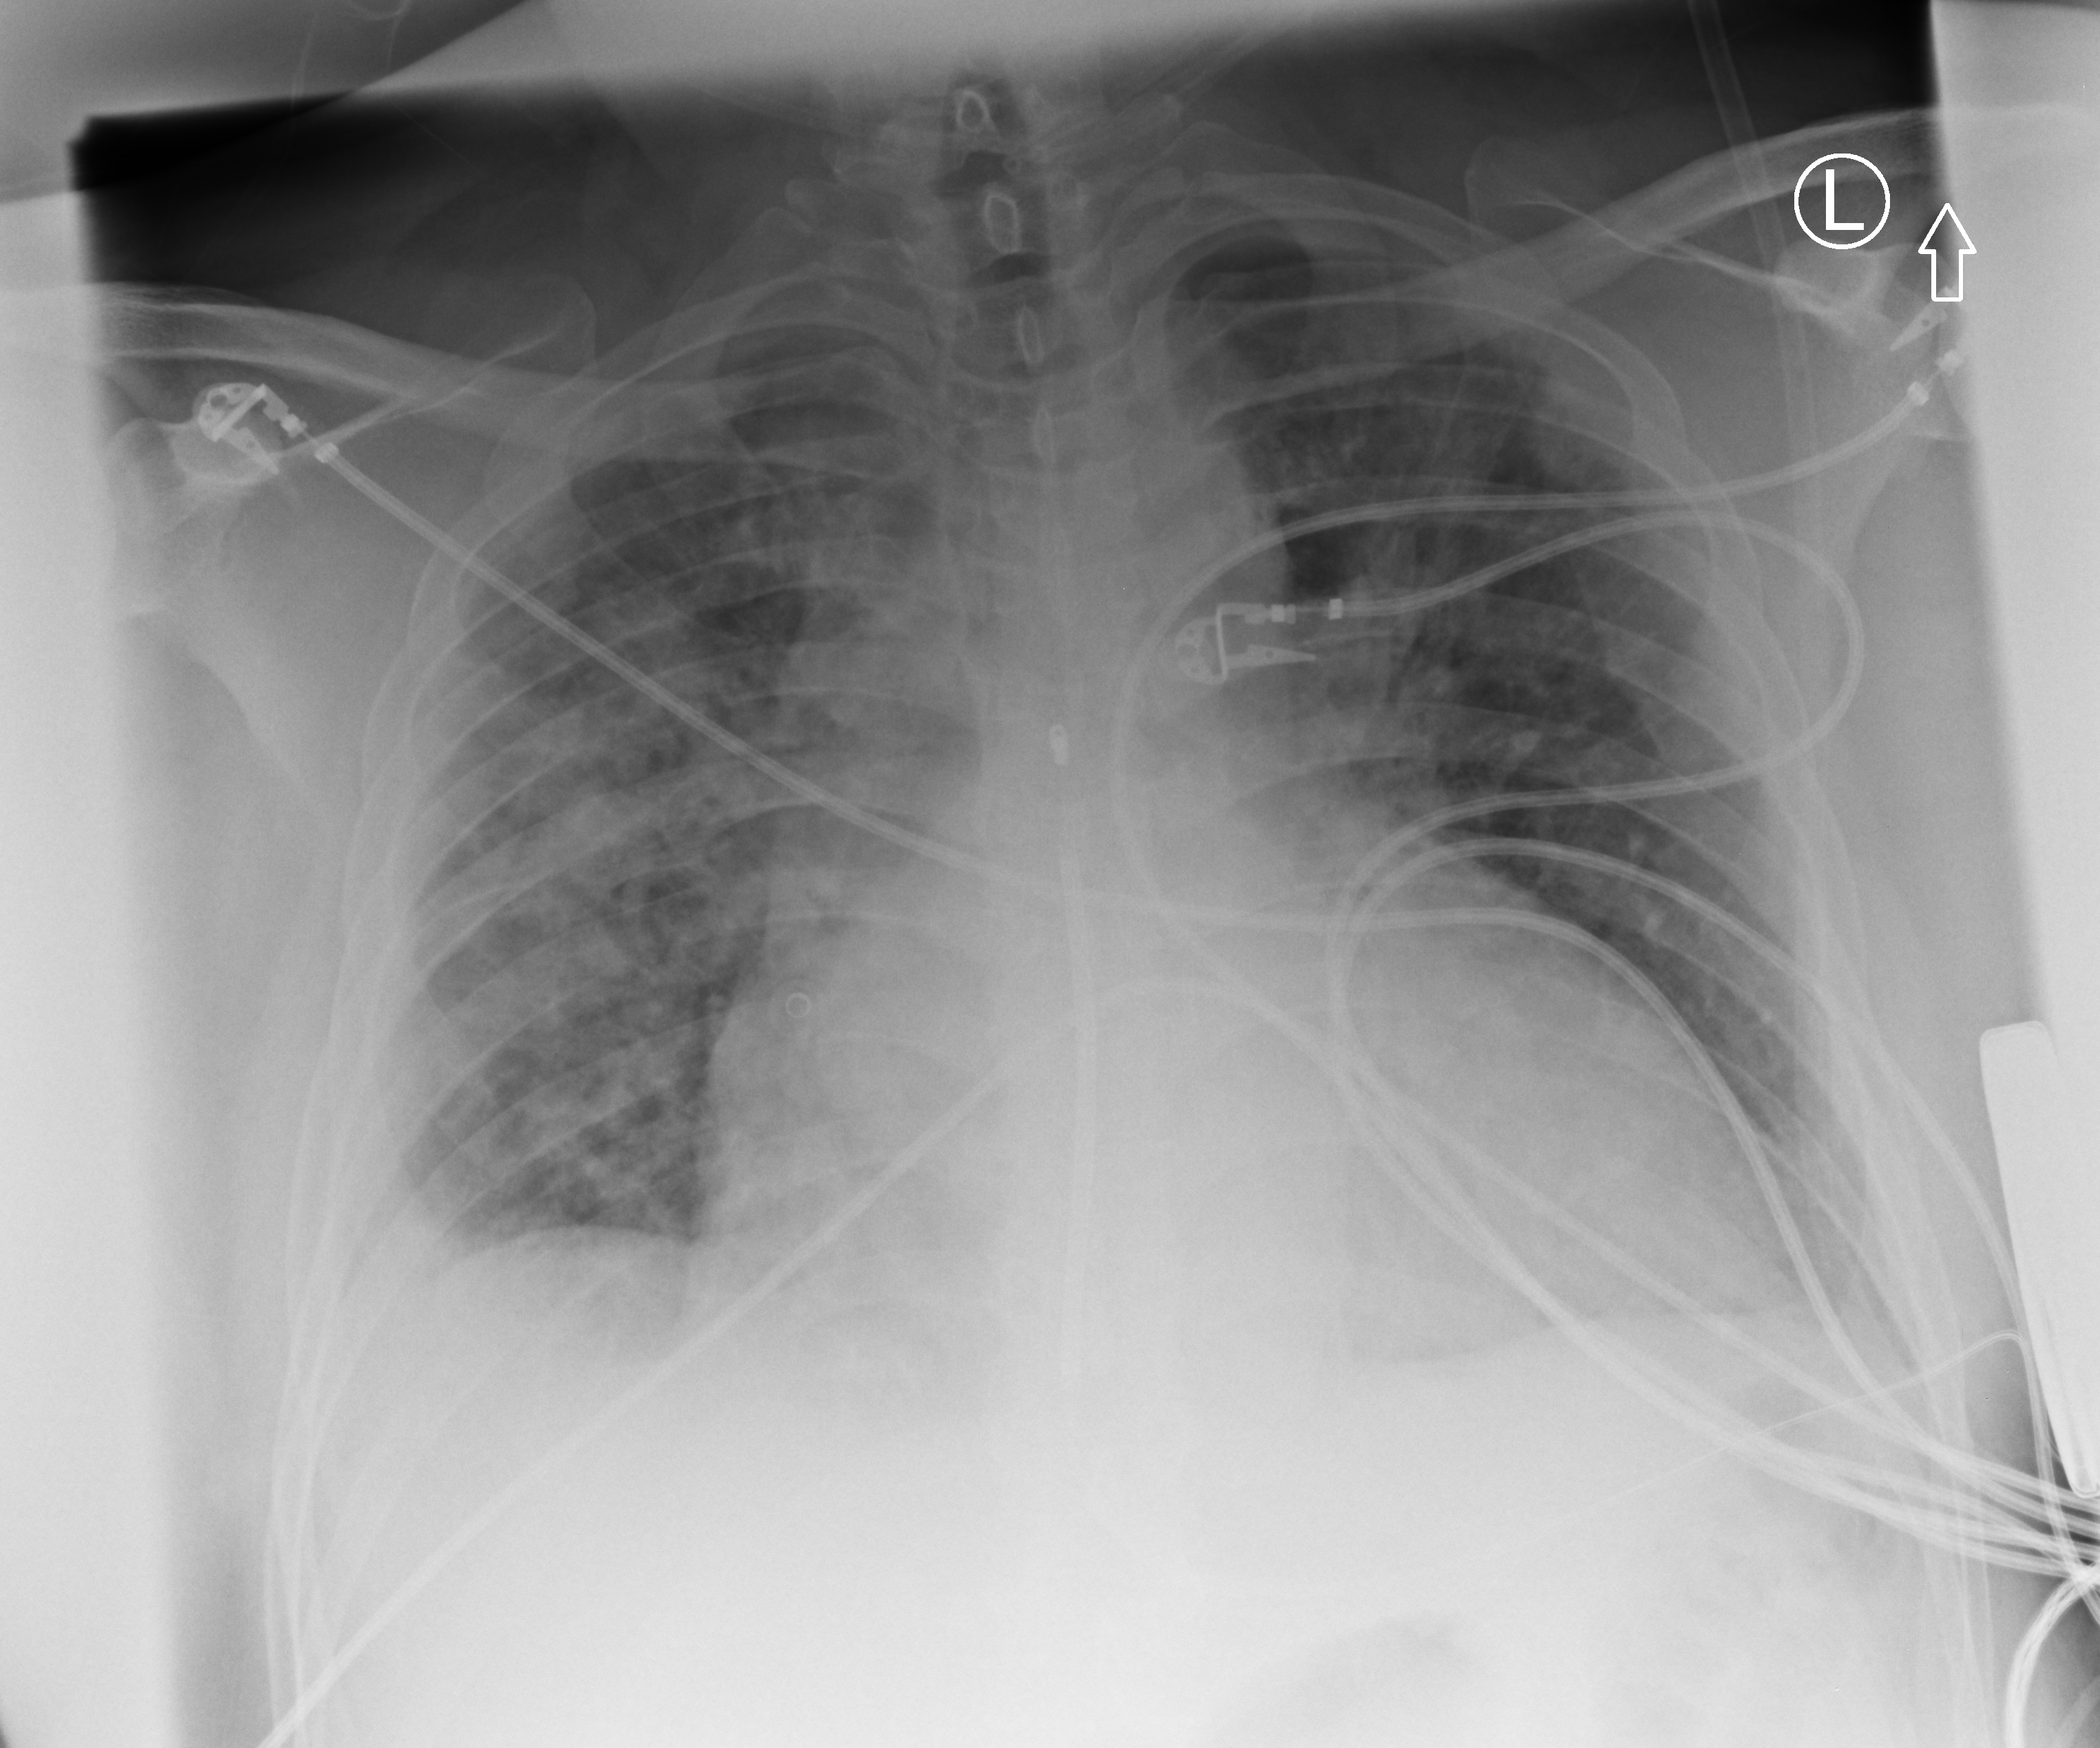
Chest X-ray (portable), anteroposterior (AP) projection. Patient hospitalised with COVID-19; male, aged 18–59 years.
Admission-level facts for this patient (not findings on this image; timing relative to this image not recorded):
- mechanically ventilated during this hospital stay: no
- admitted to intensive care during this hospital stay: no
- length of hospital stay: 19 days